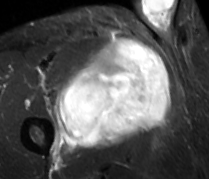
MRI of an extremity soft-tissue mass, one axial slice. Slice 52 of 89 in the series (ordered by position). STIR. MR volume resampled by the dataset authors to the PET/CT grid (not the native acquisition matrix). 3.27 mm slice thickness. 209 × 179 image matrix, field of view 204 × 175 mm. Male patient. From the clinical record (not read from this slice): histological type: undifferentiated - pleiomorphic; grade: high; site of the primary tumour: right thigh.
Annotated regions visible in this slice (expert contour drawn on MRI and transferred to this co-registered scan by the dataset authors):
- gross tumour volume including surrounding oedema: box from (x=53, y=37) to (x=170, y=150) px
- gross tumour volume (mass): (x=59, y=39)–(x=170, y=149)